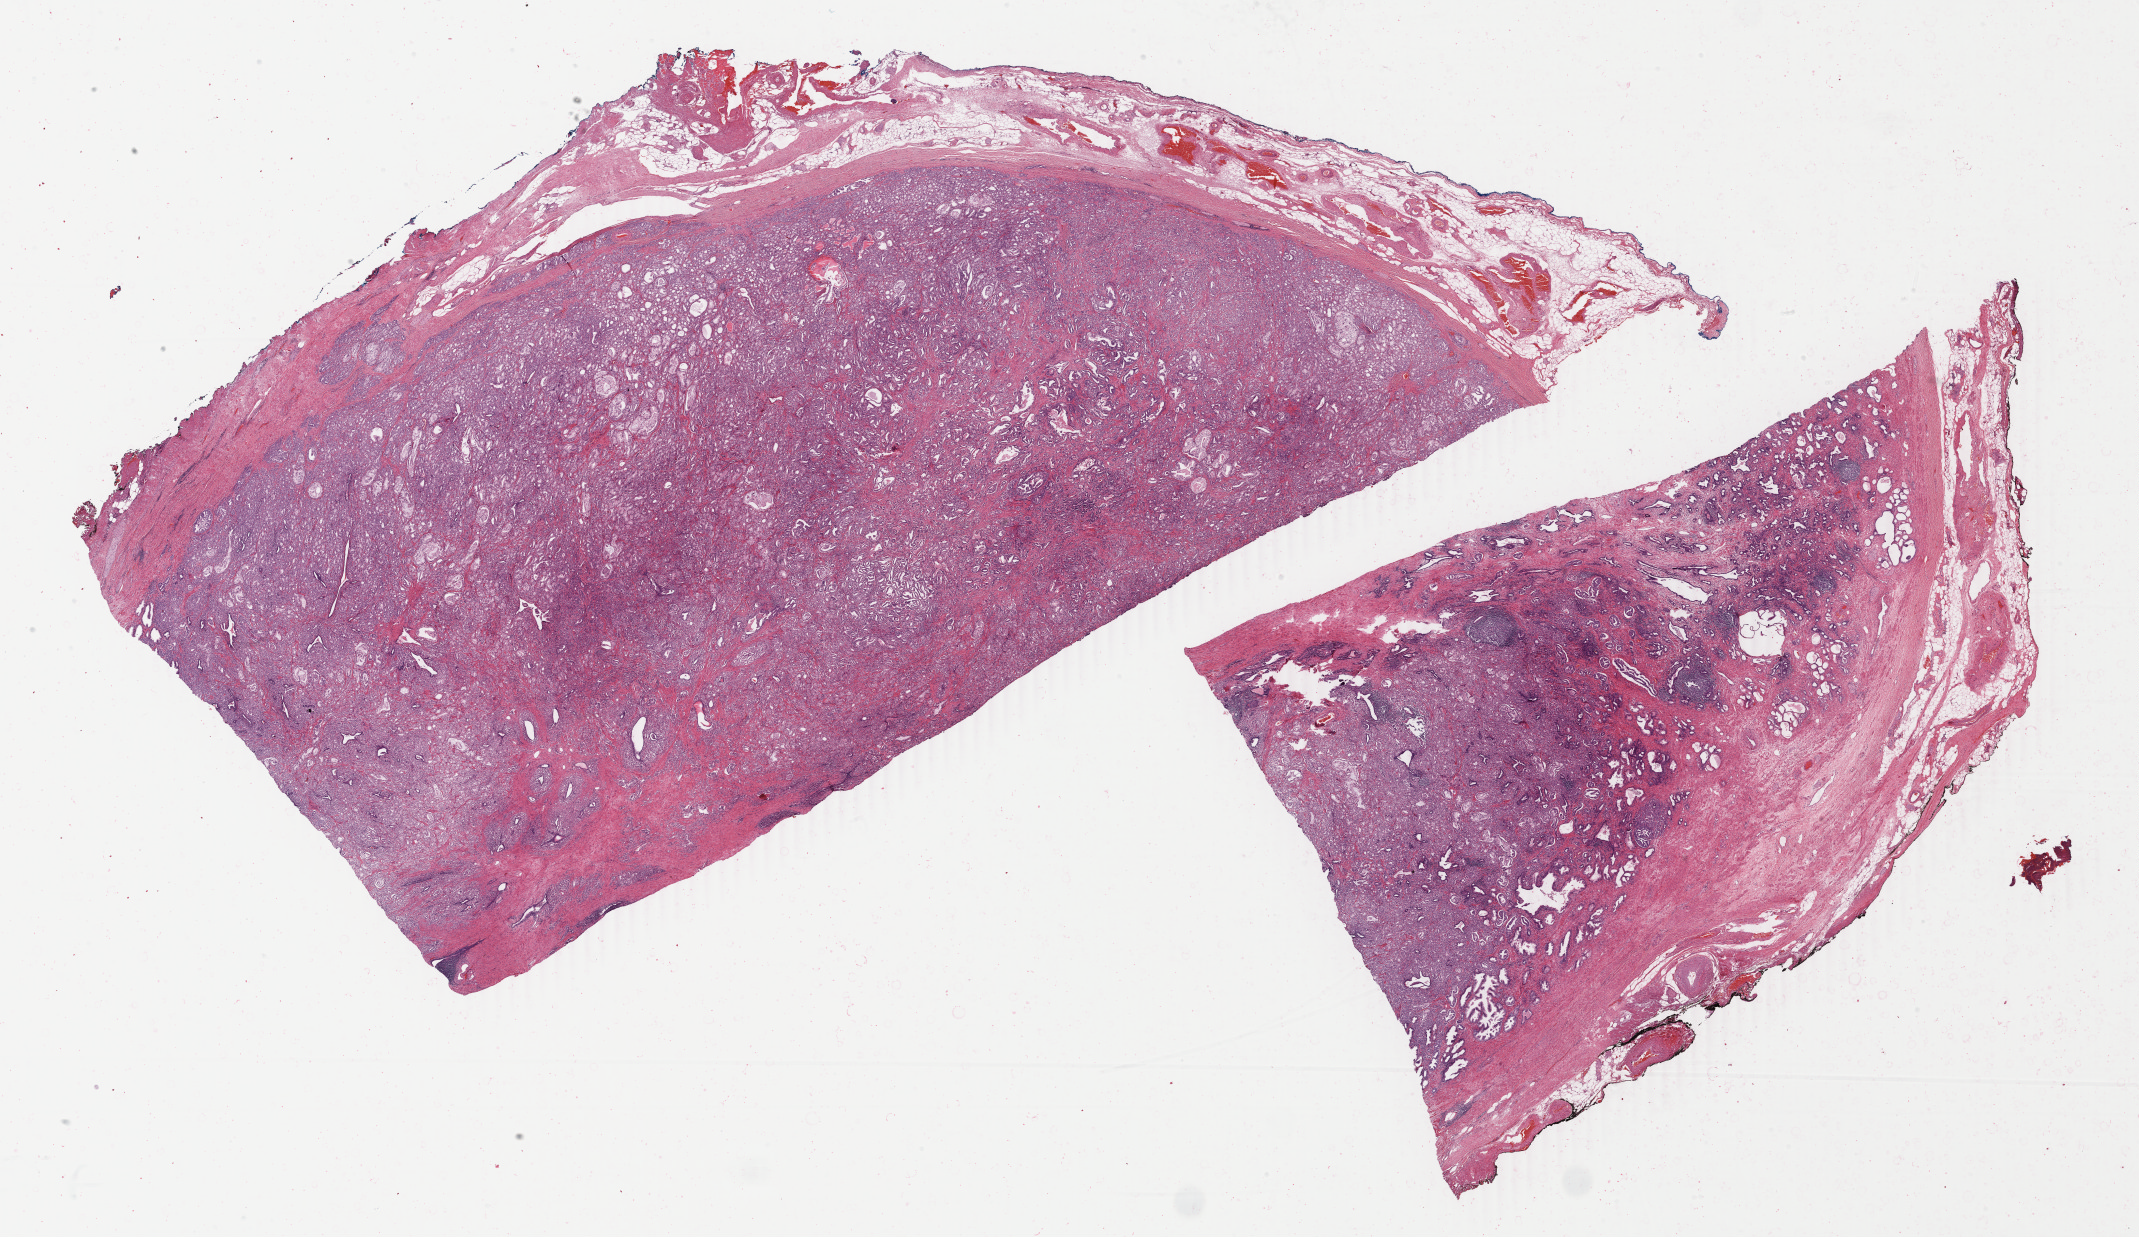
Whole-slide histology image, H&E-stained — whole scanned area (about 34.0 x 19.7 mm) shown as a low-resolution overview, formalin-fixed paraffin-embedded (FFPE) diagnostic section, prostate, primary tumour sample. Male patient; age at initial diagnosis 68 years. Gleason score: 8 (4+4).
Diagnosis: Adenocarcinoma, NOS (prostate gland). Lymph nodes positive (case pathology): 0 of 2 examined.